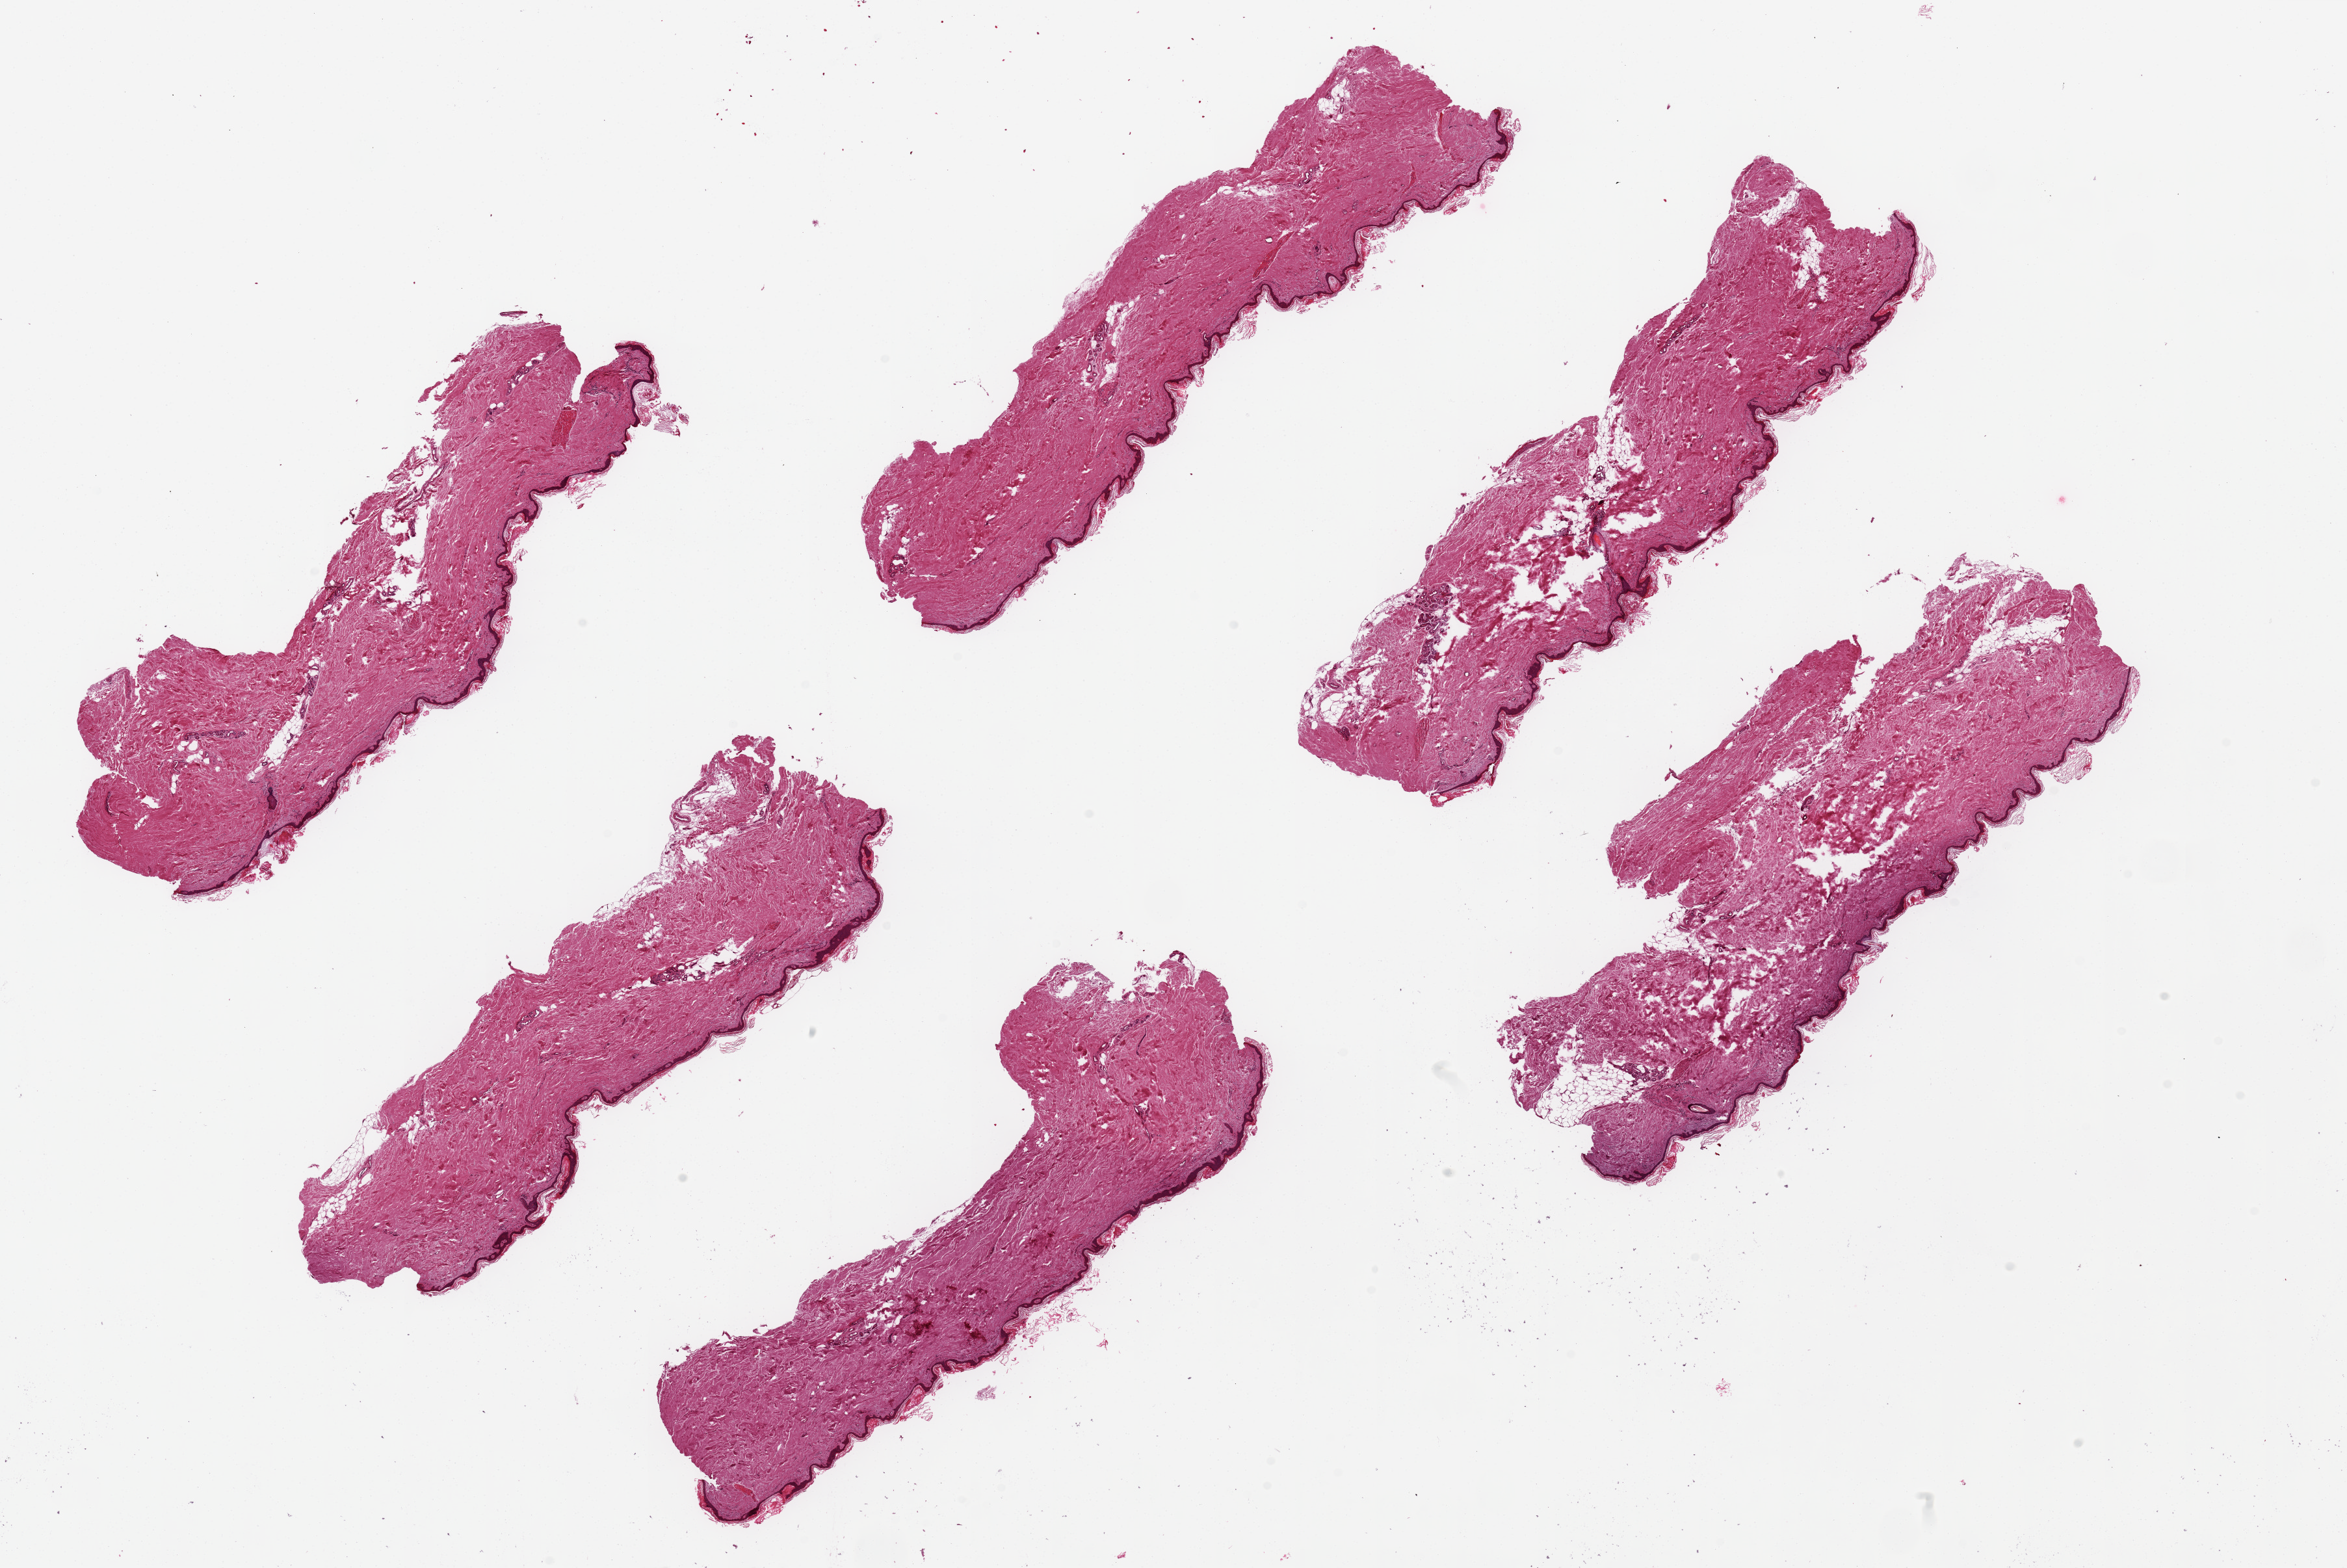
Haematoxylin and eosin whole-slide image, low-resolution overview of the scanned area, about 28.5 x 19.1 mm (slide scanned at 20x); PAXgene-fixed, paraffin-embedded tissue; section of skin of lower leg (target tissue); donor tissue sample. Donor sex: male.
• pathologist's review note for this sample: 6 pieces up to 9x3 mm; moderate tissue tears